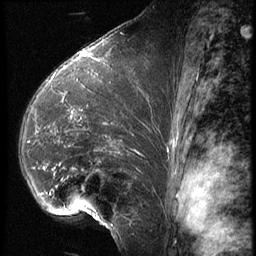
Breast MRI (dynamic contrast-enhanced), one sagittal slice; position 37 of 62 along the scan axis; 3 images stored at this slice position (order not interpretable as contrast timing); 1.5 T; TE 4.2 ms, TR 9 ms; 2.5 mm slice thickness; 256 × 256 image matrix, field of view 180 × 180 mm. Female patient, age 39 years. Case-level facts recorded for this patient, not image findings: setting: breast cancer imaged before/during neoadjuvant chemotherapy; receptor status: HER2-positive.
Annotated regions visible in this slice (semi-automatic segmentation, software-assisted and operator-edited):
- analysis volume of interest (the breast-tissue region the enhancement analysis was run in; not a lesion): bounding box <19,64,159,228> (left, top, right, bottom; pixels)
- tumour enhancement mask (voxels above the 140 % enhancement threshold inside the analysis volume of interest): <43,122,115,215>